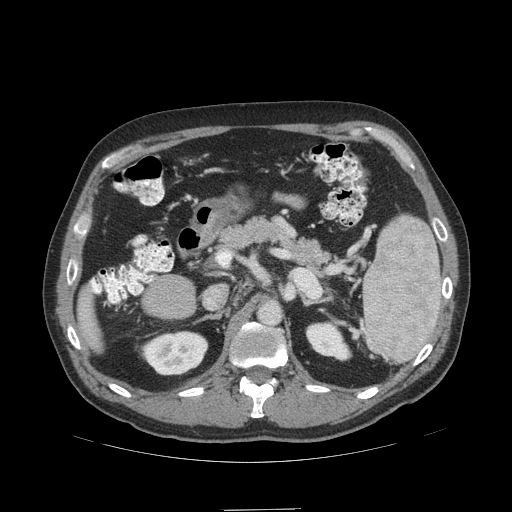
Contrast-enhanced abdominal CT (liver protocol), one axial slice. Position 57 of 99 along the scan axis. 140 kVp. Soft-tissue window (W 400 / L 40 HU). 512 × 512 image matrix, field of view 440 × 440 mm. Case-level facts recorded for this patient, not image findings: diagnosis: hepatocellular carcinoma (patient treated with transarterial chemoembolisation; whether this scan precedes or follows treatment is not stated here); TNM stage (as recorded): Stage-I; Child-Pugh class: A; tumour differentiation: no biopsy; tumour nodularity: uninodular.
Annotated regions visible in this slice (semi-automatically segmented with operator editing):
- liver parenchyma outside the tumour (the mass and vessels are separate outlines, so this box may not span the whole liver): bounding box (x1, y1, x2, y2) in pixels: (77, 286, 104, 352)